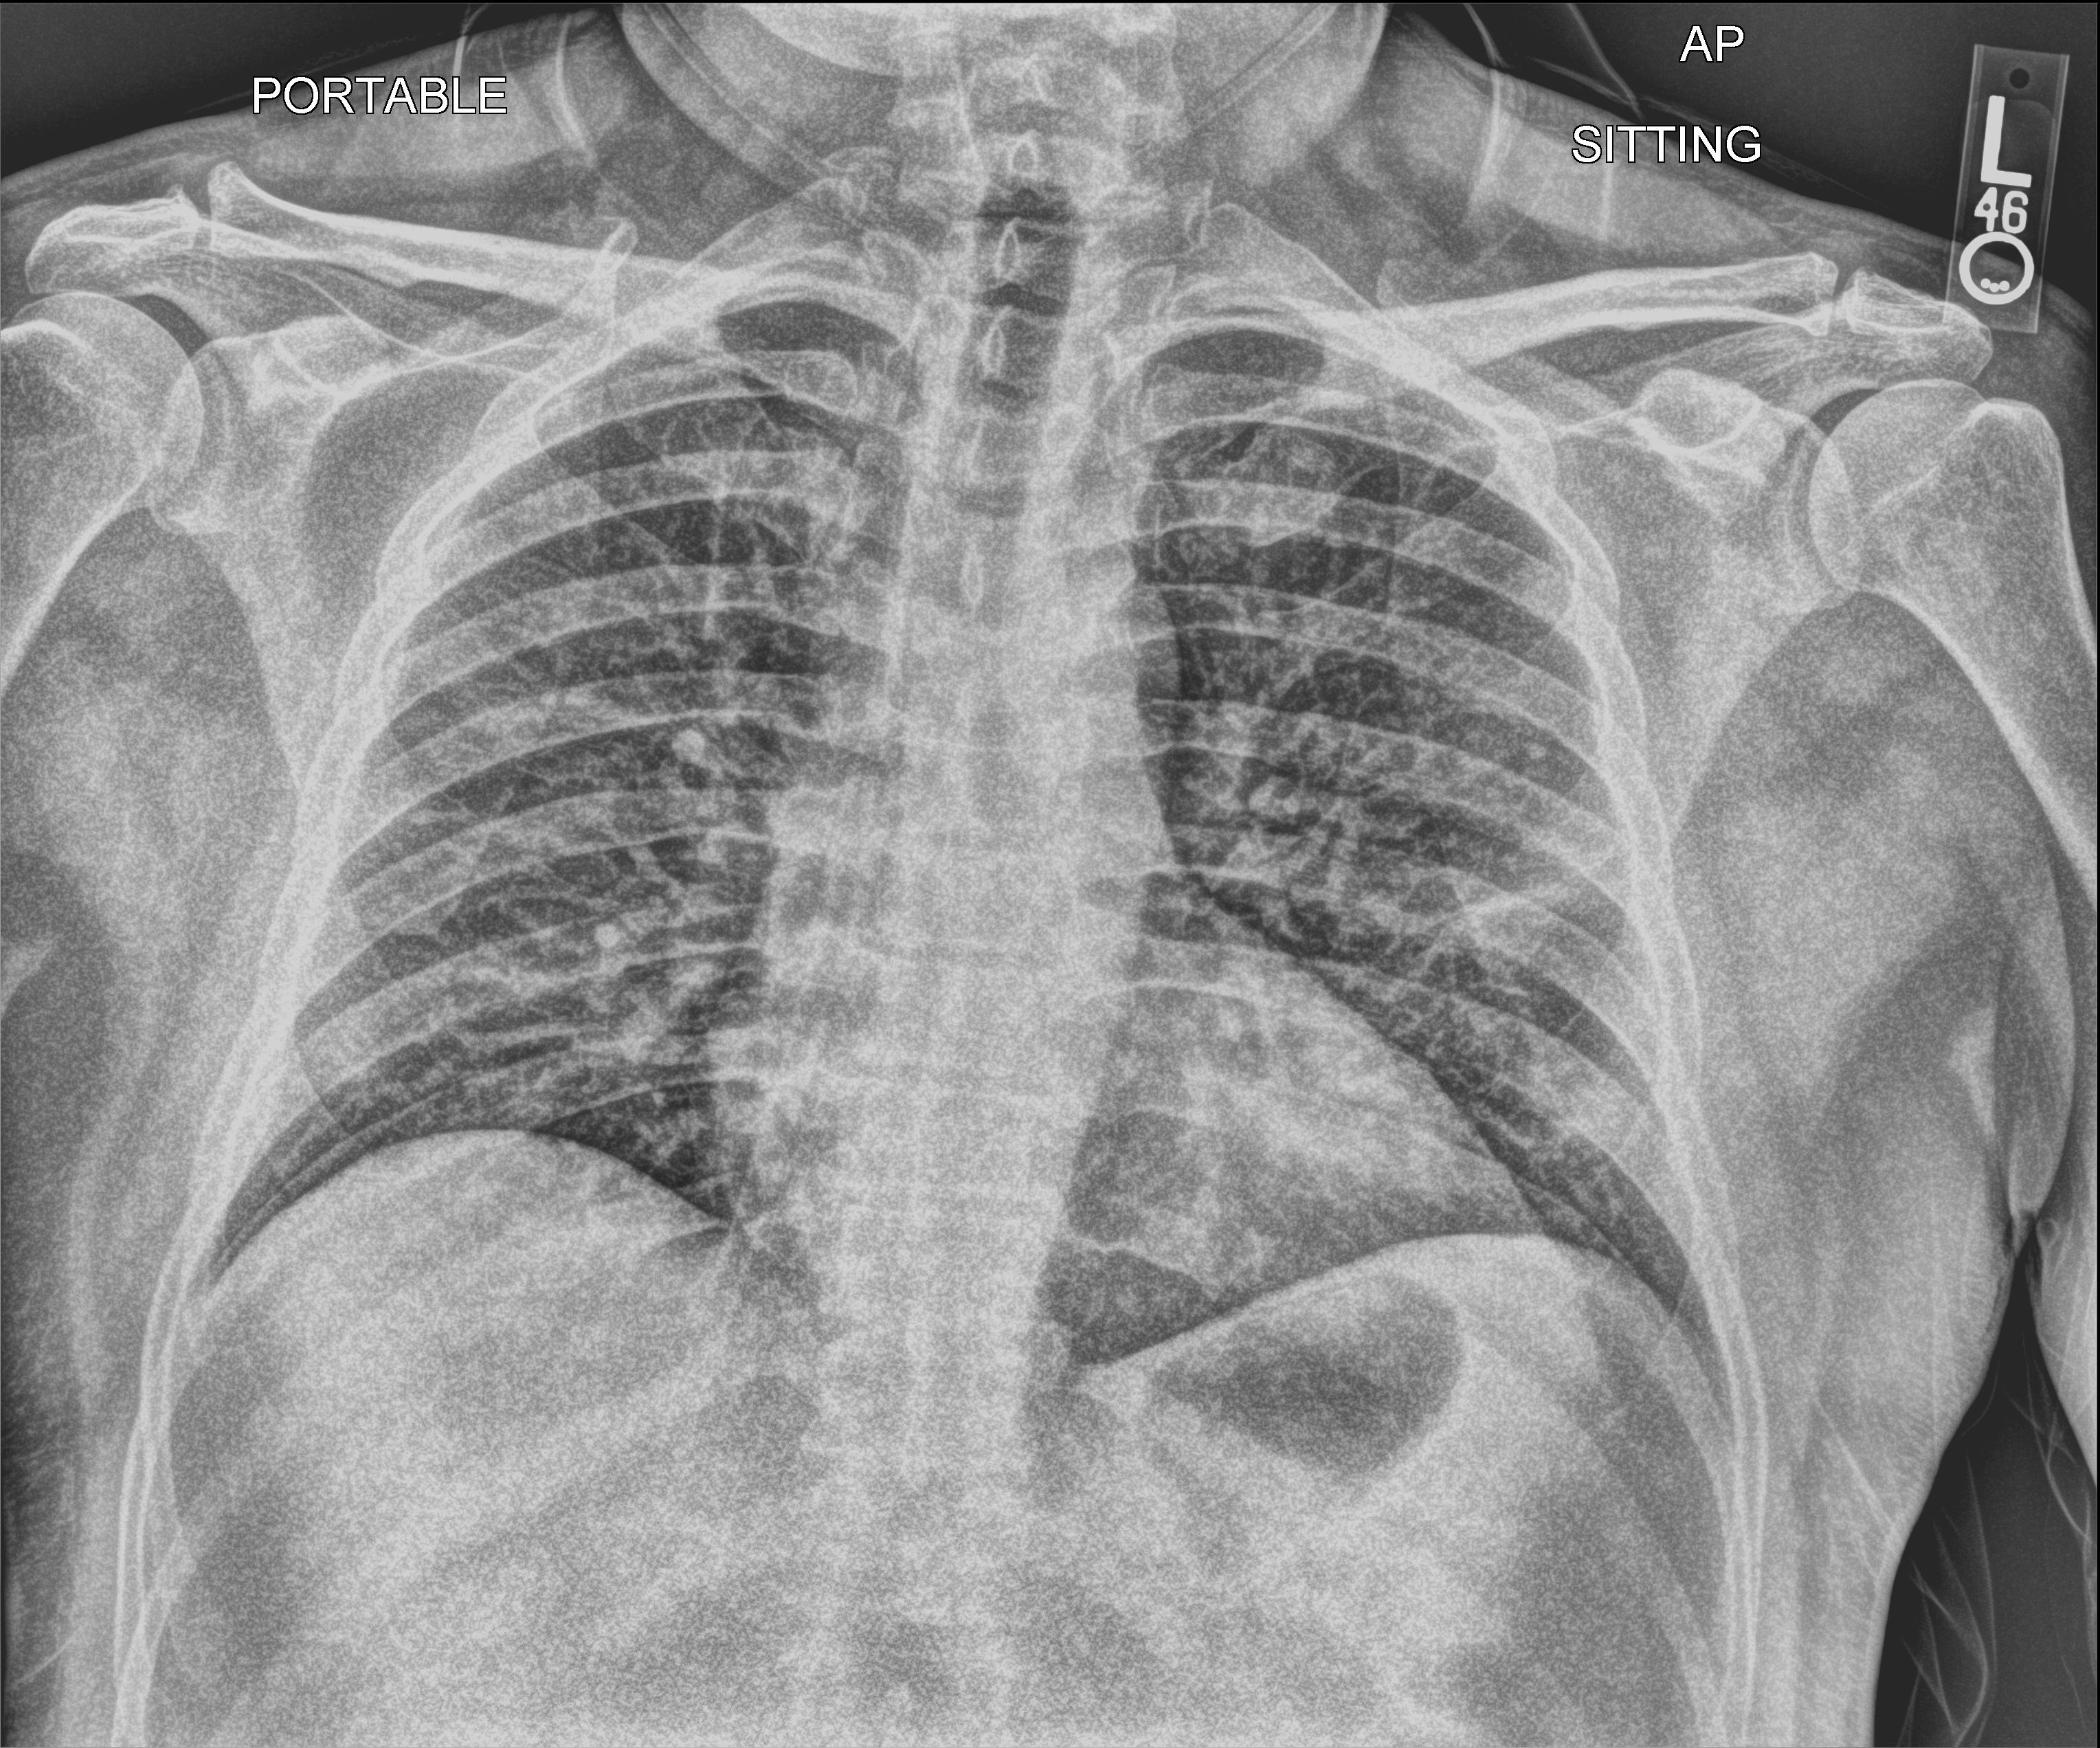
Bedside chest radiograph (computed radiography); anteroposterior (AP) projection. Patient hospitalised with COVID-19; male, aged 18–59 years.
Admission-level facts for this patient (not findings on this image; timing relative to this image not recorded): hypertension (admission record): no; diabetes (admission record): no; mechanically ventilated during this hospital stay: yes.